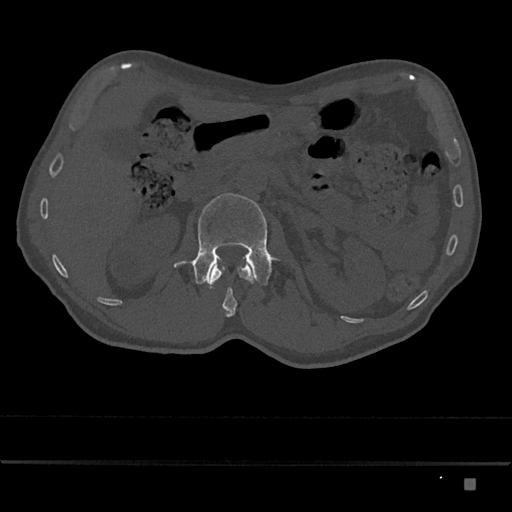
CT including the spine, one axial slice; position 500 of 797 along the scan axis; bone window (W 1800 / L 400 HU); 0.5 mm slice thickness; 512 × 512 image matrix, field of view 390 × 390 mm. Male patient, age 72 years. From the clinical record (not read from this slice): primary cancer: prostate.
Outlined on this slice (semi-automatic segmentation, software-assisted and operator-edited):
- L1 vertebra: bounding box (x1, y1, x2, y2) in pixels: (207, 258, 255, 317)
- L2 vertebra: (174, 193, 278, 286)